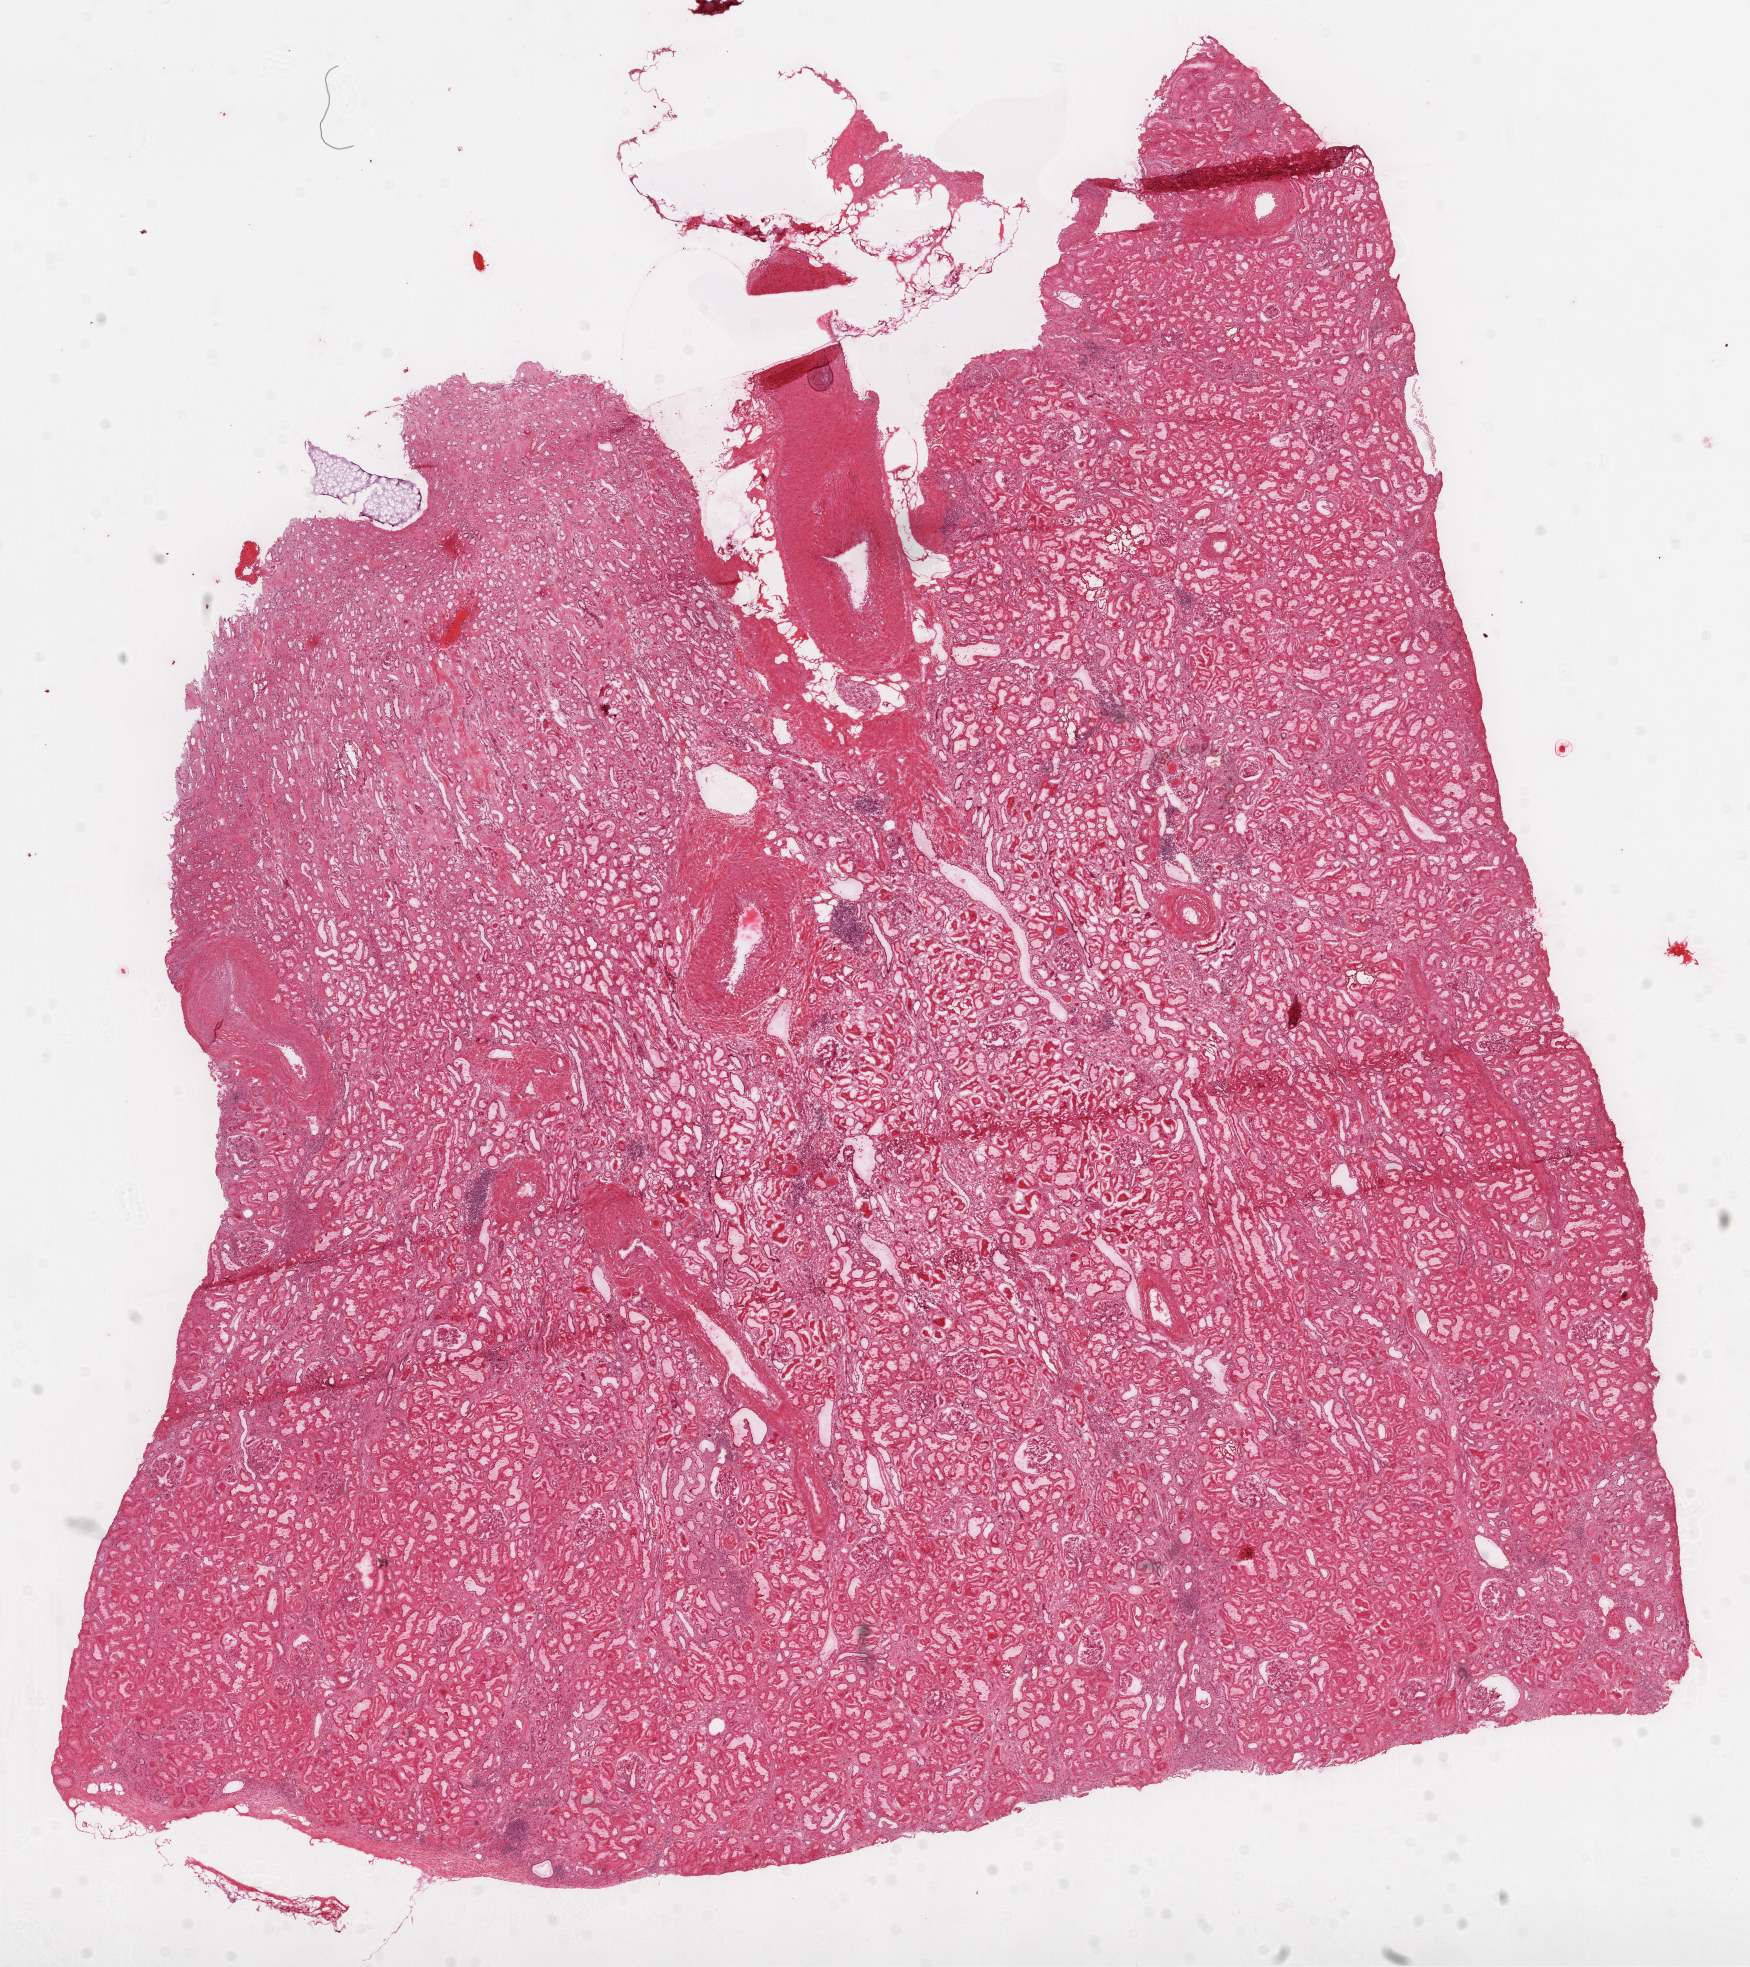
Whole-slide histology image, Hematoxylin and eosin (H&E) stained — whole scanned area (about 14.0 x 15.8 mm) shown as a low-resolution overview; frozen section; solid tissue normal (non-tumour tissue) sample from the kidney. Patient: male, age at initial diagnosis 79 years.
This section: solid tissue normal (non-tumour) sample from the same patient. Patient diagnosis: Clear cell adenocarcinoma, NOS.